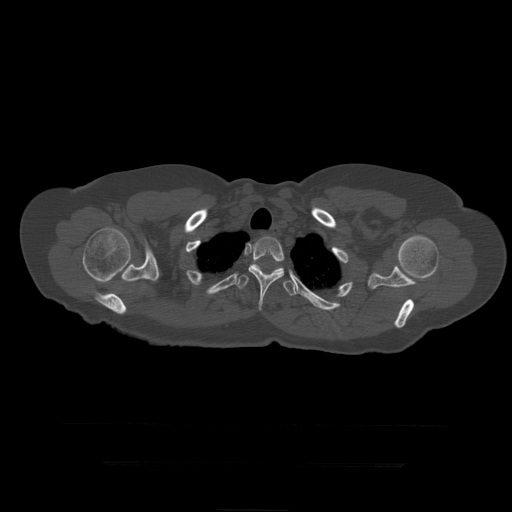
CT including the spine, one axial slice. Position 360 of 399 along the scan axis. Bone window (W 1800 / L 400 HU). 512 × 512 image matrix, field of view 450 × 450 mm. Patient age 41 years. From the clinical record (not read from this slice): primary cancer: breast.
Structures marked on this image (semi-automatically segmented with operator editing):
- T3 vertebra: bounding box <249,237,285,311> (left, top, right, bottom; pixels)
- T4 vertebra: <235,264,297,296>